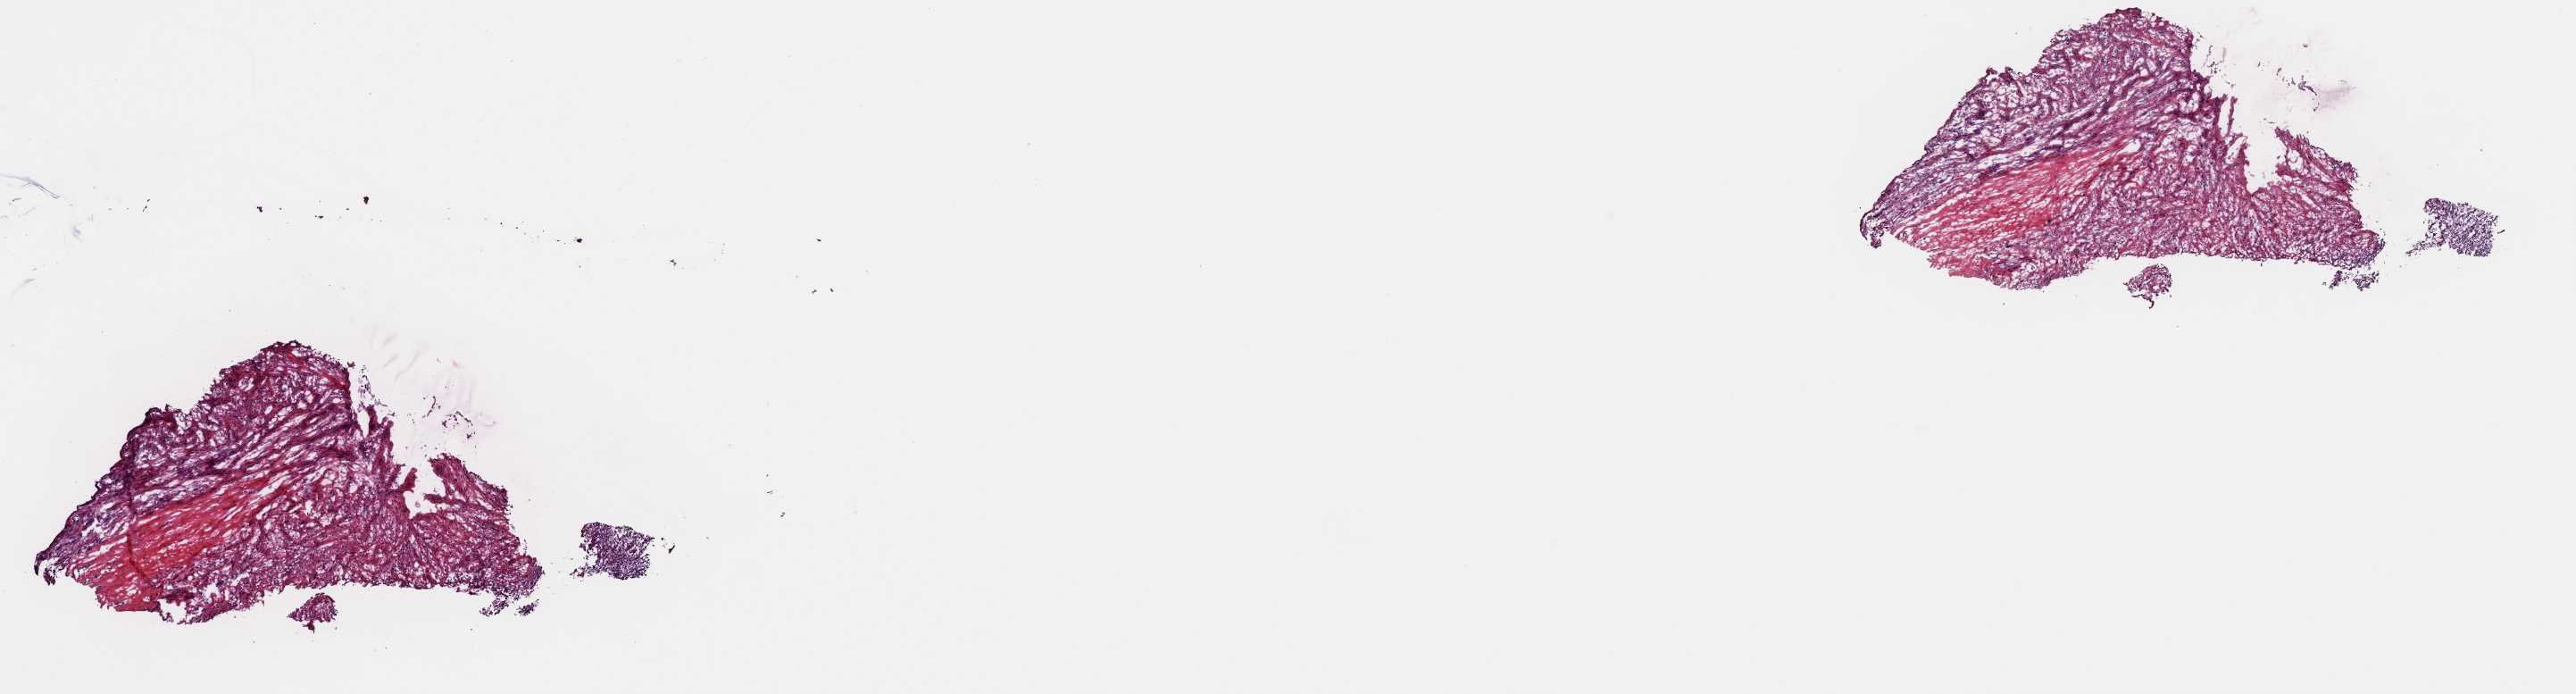
Whole-slide histology image, H&E-stained — a low-resolution overview of the entire scanned area, about 22.8 x 6.1 mm (acquisition: 40x scan), frozen section from the top of the tissue portion, primary tumour sample from the connective, subcutaneous and other soft tissues. Patient: male, age at initial diagnosis 65 years. Slide review estimates, as recorded: tumour cells 80%, tumour nuclei 94%, normal cells 0%, stromal cells 20%, necrosis 0%. Infiltration values recorded for this section: lymphocyte infiltration 0%, monocyte infiltration 0%, neutrophil infiltration 0%.
• histologic diagnosis: Leiomyosarcoma, NOS (connective, subcutaneous and other soft tissues of lower limb and hip)